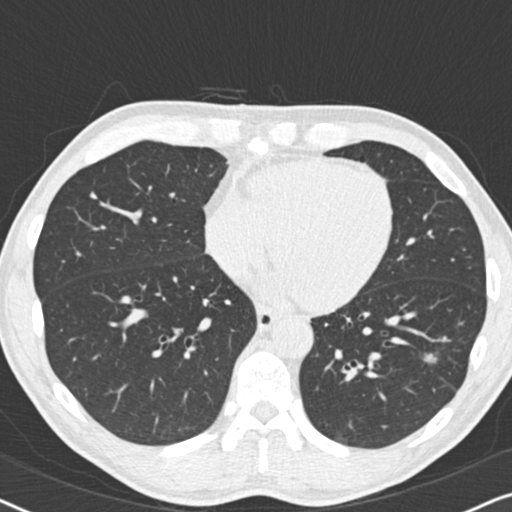
Chest CT (low-dose screening protocol), one axial image. Second annual screen. Lung window (W 1500 / L -600 HU). 2 mm slice thickness. 120 kVp. Slice 124 of 208 in the series. Male, age 59 years at enrolment. Current smoker at enrolment.
Expert-annotated lung lesion, bounding box (x1, y1, x2, y2) in pixels: (414, 338, 459, 380). The screening reader recorded 2 non-calcified nodules or masses ≥4 mm on this exam (left lower lobe, right middle lobe); which of them this box marks is not recorded. Official screen result: positive, other. Later outcome: lung cancer diagnosed 484 days after this screen (after the third annual screen) — adenocarcinoma, NOS, left lower lobe, poorly differentiated (G3), stage IA (AJCC 6th edition), 20 mm at pathology.